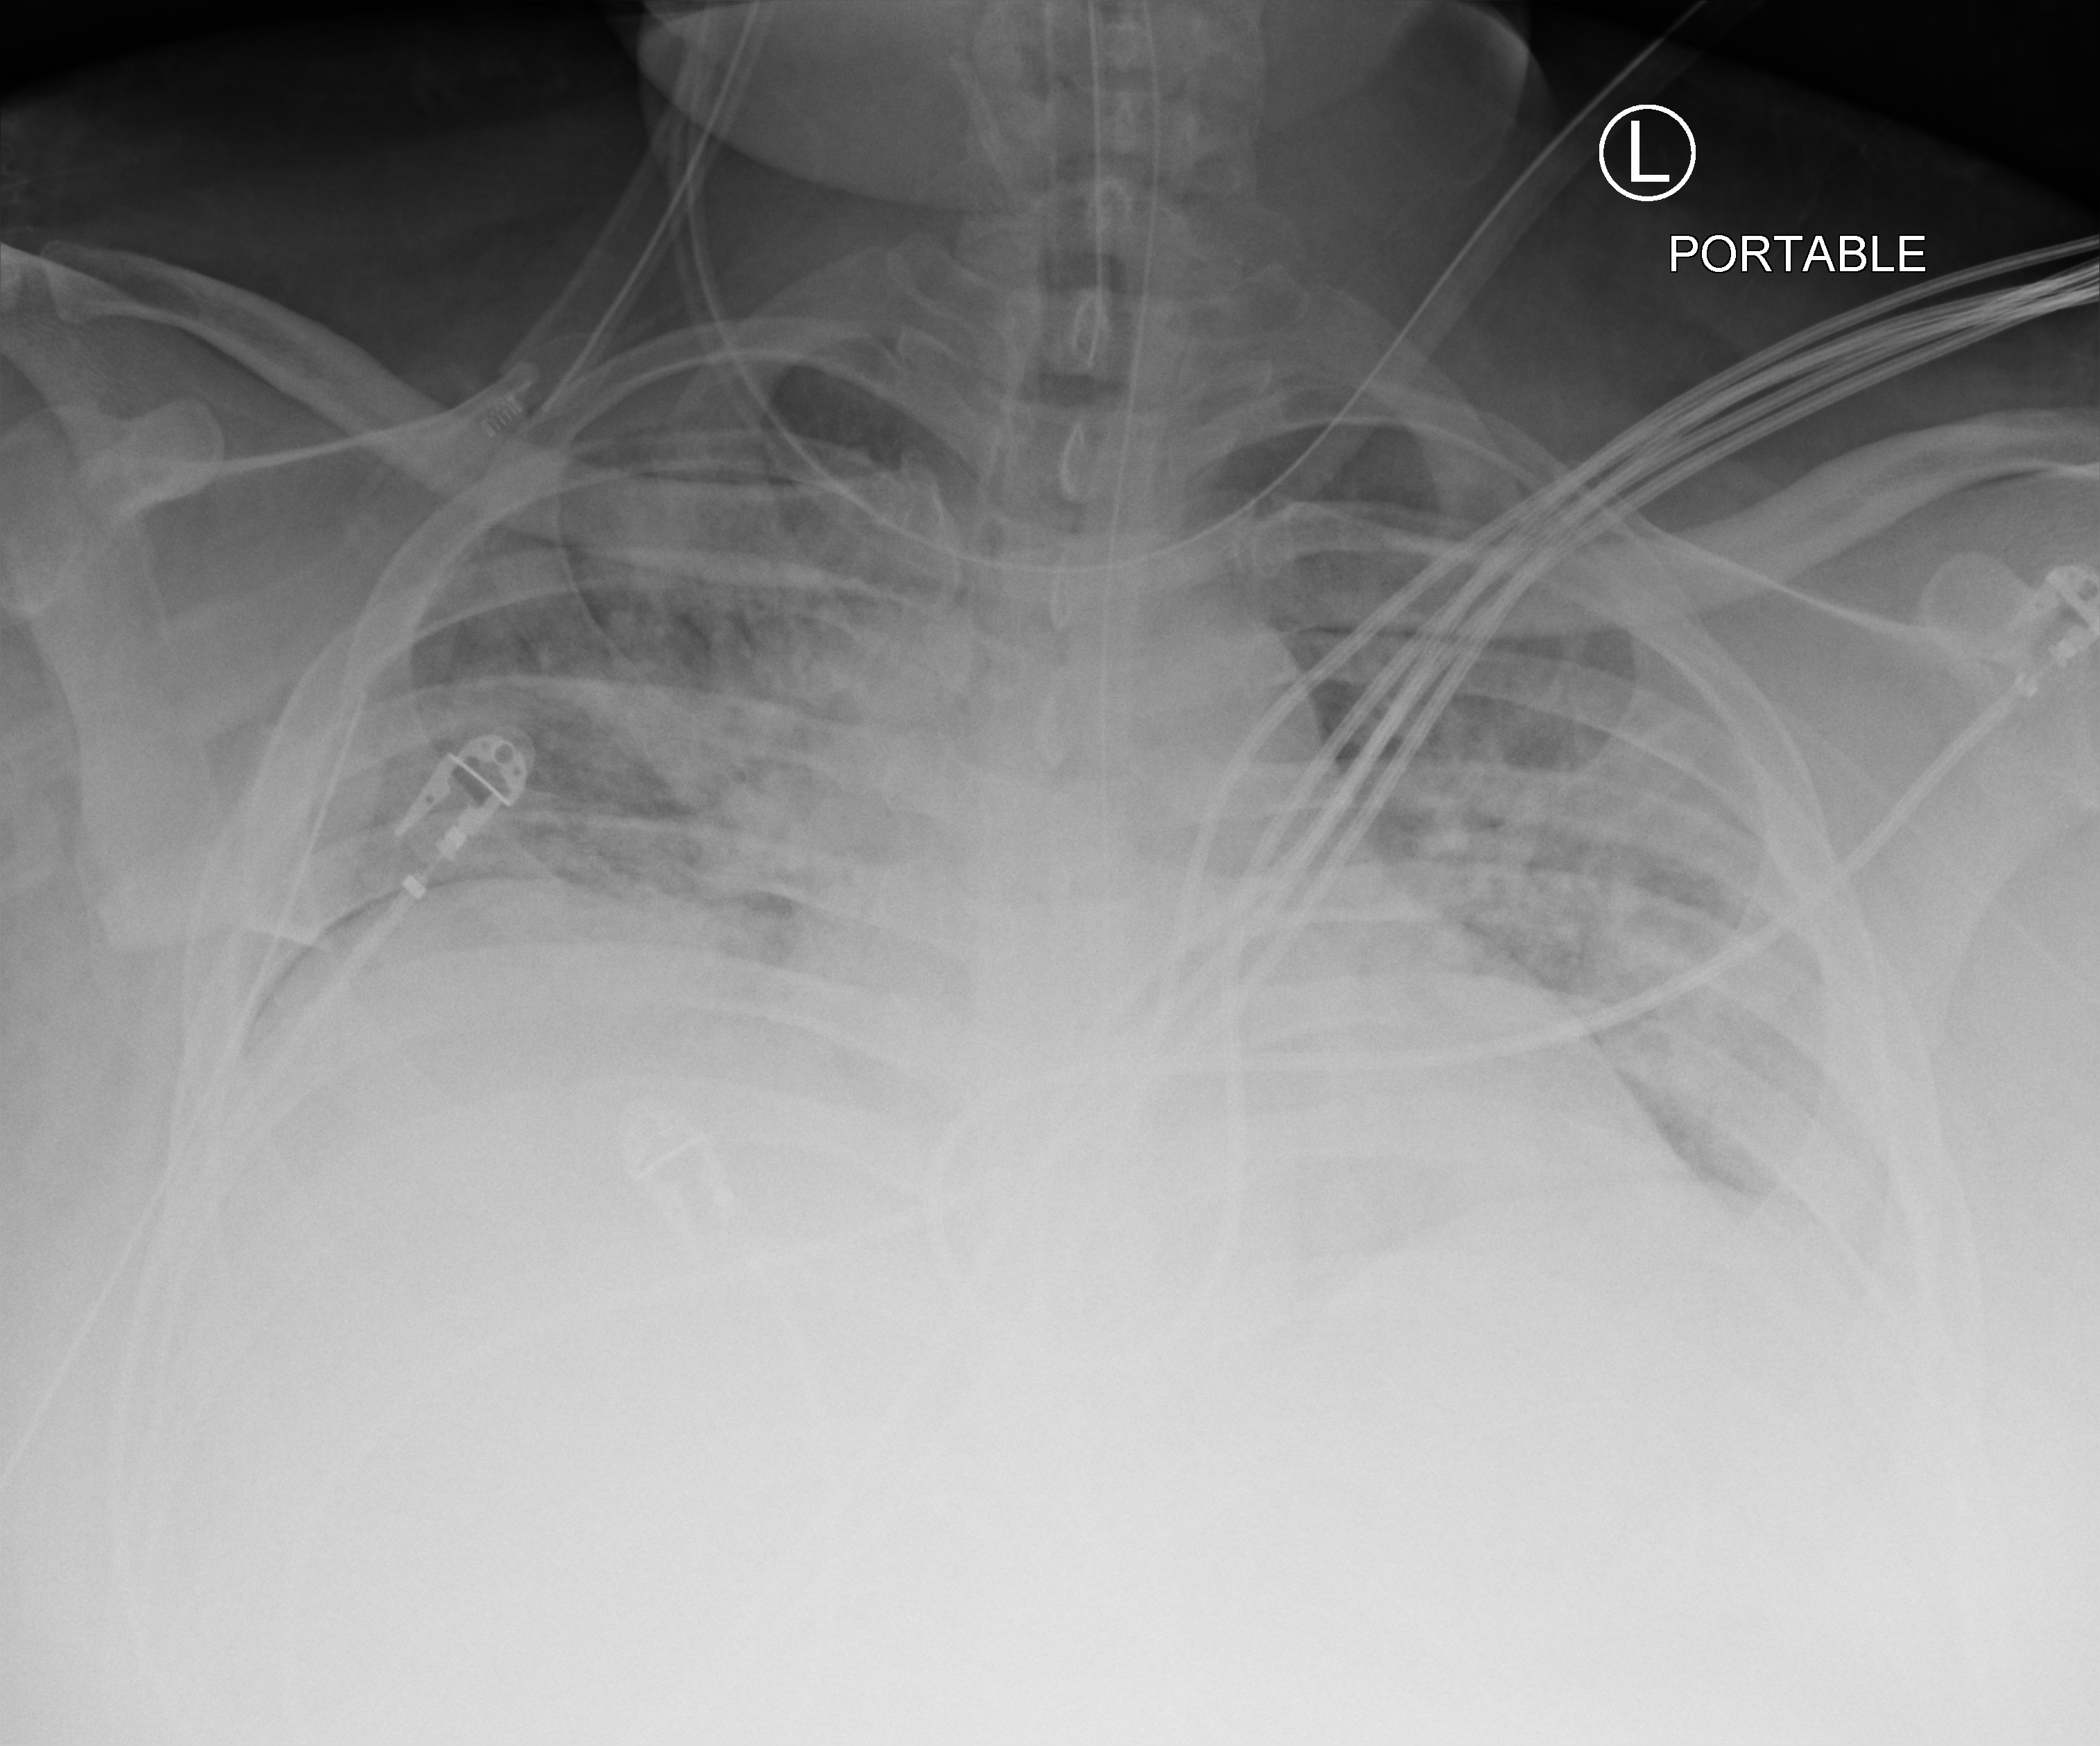
Bedside chest radiograph (computed radiography), anteroposterior (AP) projection. Male patient hospitalised with COVID-19, age 18–59 years.
Hospital-stay facts (about this admission, not read from this image; timing relative to this image not recorded): other chronic lung disease (admission record): yes.